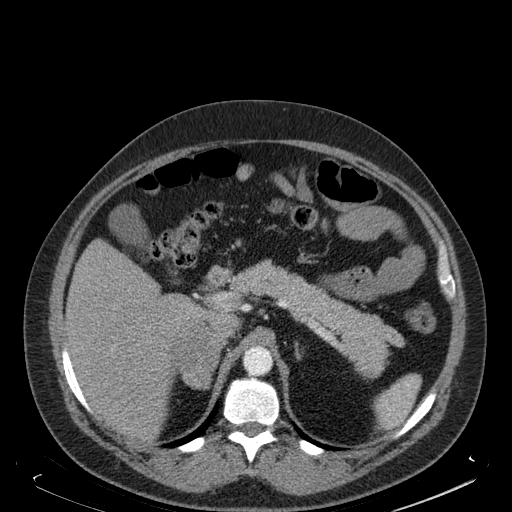
Contrast-enhanced abdominal CT, one axial slice. Position 121 of 181 along the scan axis. Soft-tissue window (W 400 / L 40 HU). 1.5 mm slice thickness. 512 × 512 image matrix, field of view 405 × 405 mm. Male patient. Case-level facts recorded for this patient, not image findings: diagnosis: adrenocortical carcinoma; tumour side: right adrenal; tumour size at pathology: 7.5 cm; Ki-67 index: 25 %; stage (as recorded): 4.
Annotated regions visible in this slice (semi-automatically segmented with operator editing):
- mass: box from (x=176, y=326) to (x=219, y=386) px